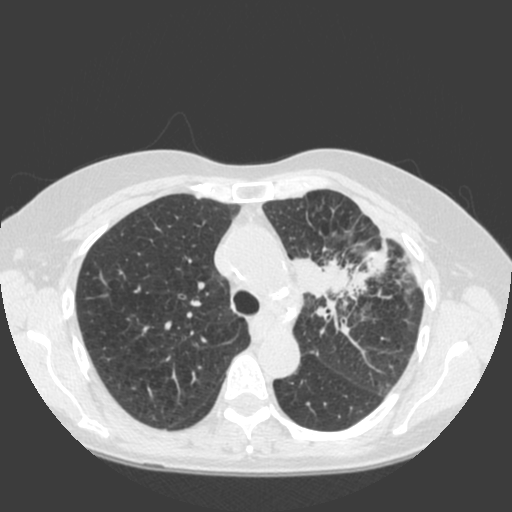
Low-dose screening chest CT, one axial slice. Slice 135 of 184 in the series (ordered by position). 120 kVp. Lung window (W 1500 / L -600 HU). 2 mm slice thickness. 512 × 512 image matrix, field of view 350 × 350 mm.
Annotated regions visible in this slice (outlined manually by an expert reader):
- lesion 1 (tumor, hilum of left lung): bounding box <291,243,389,320> (left, top, right, bottom; pixels)